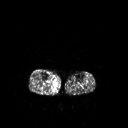
FDG PET of an extremity soft-tissue mass (from a PET/CT study), one axial slice; slice 122 of 267 in the series (ordered by position); 3.27 mm slice thickness; 128 × 128 image matrix, field of view 500 × 500 mm. Patient: male, 69 years. Case-level facts recorded for this patient, not image findings: histological type: pleiomorphic liposarcoma; grade: high; site of the primary tumour: right calf.
Annotated regions visible in this slice (expert contour drawn on MRI and transferred to this co-registered scan by the dataset authors):
- gross tumour volume including surrounding oedema: bounding box (x1, y1, x2, y2) in pixels: (52, 82, 57, 88)